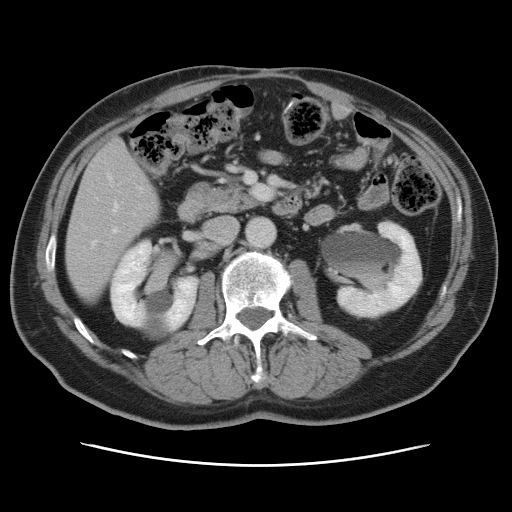
Contrast-enhanced abdominal CT, one axial slice; position 28 of 80 along the scan axis; soft-tissue window (W 400 / L 40 HU); 5 mm slice thickness; 512 × 512 image matrix, field of view 370 × 370 mm. Male patient, age 69 years. From the clinical record (not read from this slice): diagnosis: colorectal cancer liver metastases, imaged before liver resection; multiple liver metastases: no; largest metastasis: 5 cm; disease in both lobes: yes.
Annotated regions visible in this slice (expert manual segmentation):
- hepatic veins: bounding box [x1, y1, x2, y2] px = [91, 175, 118, 246]
- liver: [66, 141, 160, 298]
- planned liver remnant (the part of the liver to remain after resection): [66, 217, 136, 298]
- portal vein (with intrahepatic branches): [112, 227, 118, 233]